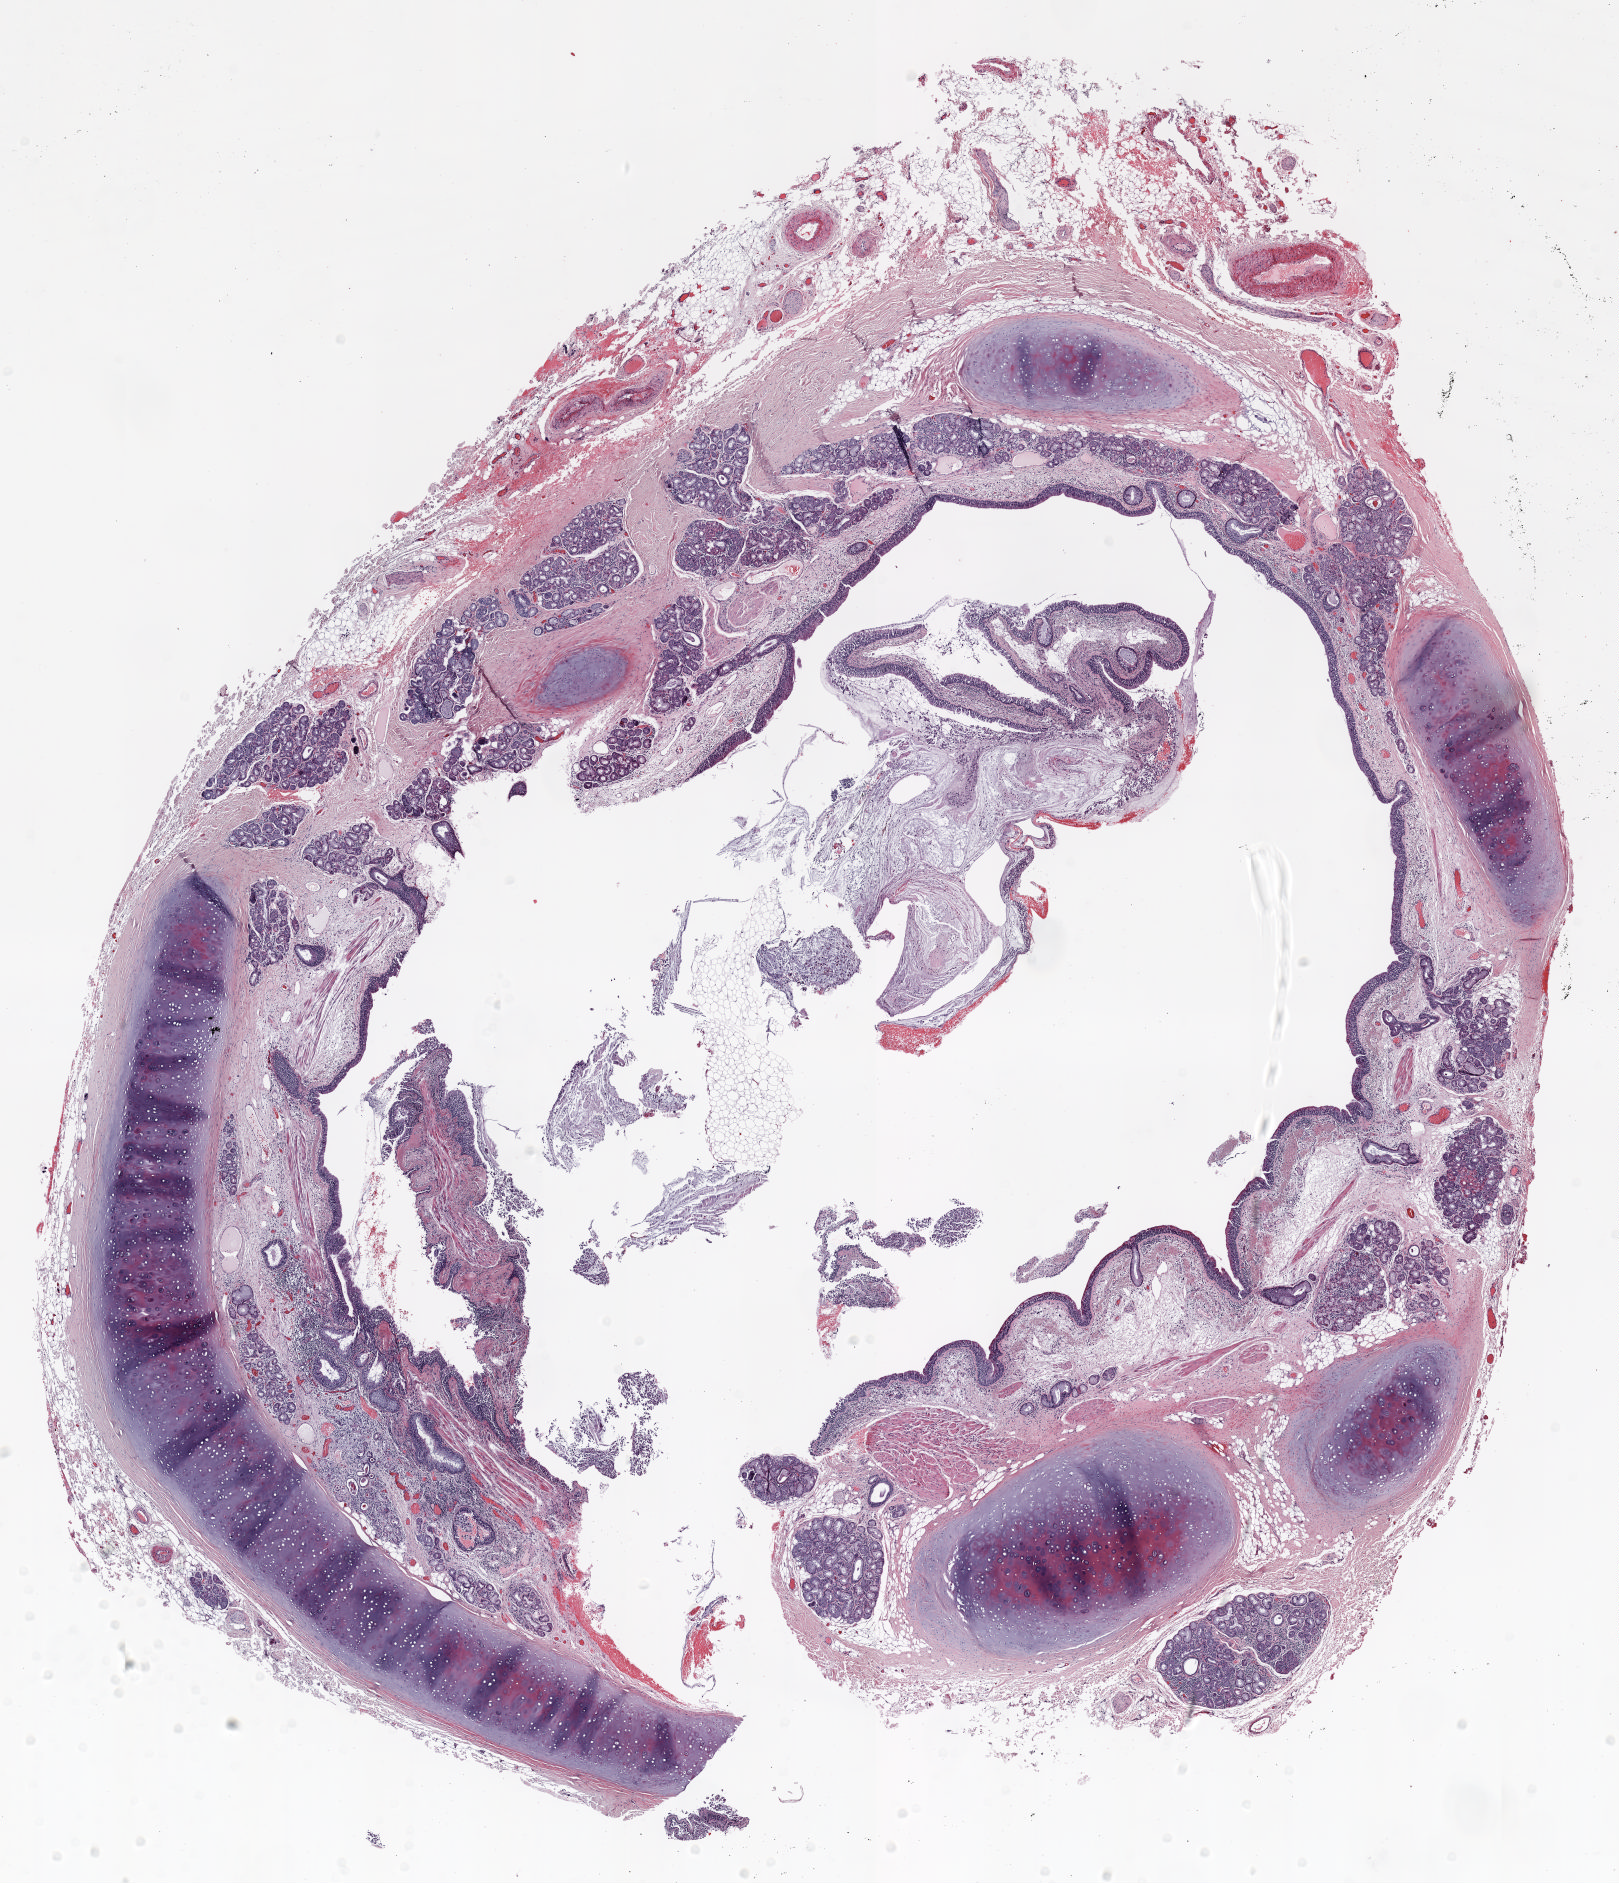
Hematoxylin and eosin (H&E) stained whole-slide image — whole scanned area (about 13.0 x 15.1 mm) shown as a low-resolution overview. FFPE section. Lung. Male patient, aged 64 at enrolment. Current smoker at enrolment. Grade: moderately differentiated (G2).
Stage (AJCC 6th edition): IA. Primary tumour location (clinical record): left upper lobe. Participant's lung-cancer diagnosis: Adenocarcinoma, NOS (ICD-O-3 8140/3). Tumour size (pathology): 29 mm.